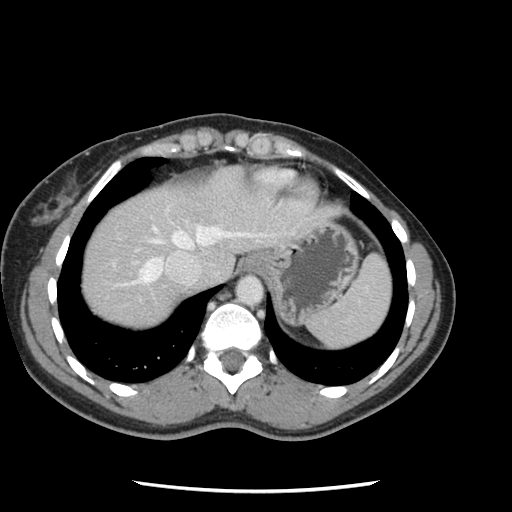
Contrast-enhanced abdominal CT, one axial slice; slice 105 of 134 in the series (ordered by position); intravenous contrast given; soft-tissue window (W 400 / L 40 HU); 512 × 512 image matrix, field of view 330 × 330 mm. Female patient, age 43 years. From the clinical record (not read from this slice): diagnosis: colorectal cancer liver metastases, imaged before liver resection; multiple liver metastases: yes; largest metastasis: 3.4 cm; disease in both lobes: yes.
Outlined on this slice (outlined manually by an expert reader):
- hepatic veins: bounding box <134,225,255,284> (left, top, right, bottom; pixels)
- liver: <82,180,301,326>
- planned liver remnant (the part of the liver to remain after resection): <82,190,201,303>
- portal vein (with intrahepatic branches): <113,249,141,265>